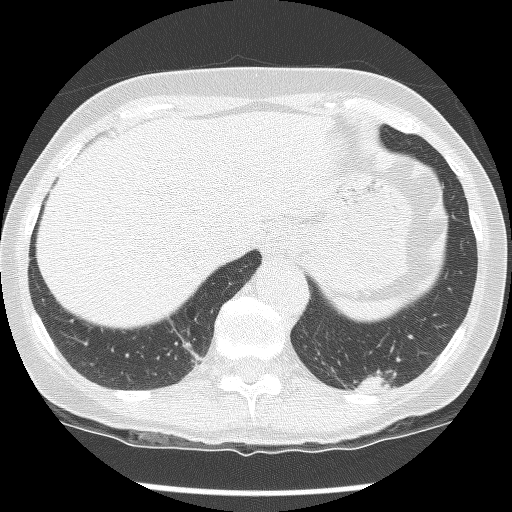
Axial slice from a low-dose chest CT screening exam, second annual screen, lung window (W 1500 / L -600 HU), slice 107 of 136 in the series. Female, age 61 years at enrolment.
• Expert-annotated lung lesion, bounding box <326,307,441,411> (left, top, right, bottom; pixels).
• The screening reader recorded 2 non-calcified nodules or masses ≥4 mm on this exam; which of them this box marks is not recorded.
• Official screen result: positive, no significant change: stable abnormalities potentially related to lung cancer, unchanged since the prior screening exam.
• Later outcome: lung cancer diagnosed 585 days after this screen — non-small cell carcinoma, left lower lobe, poorly differentiated (G3), stage IB (AJCC 6th edition), 100 mm at pathology.